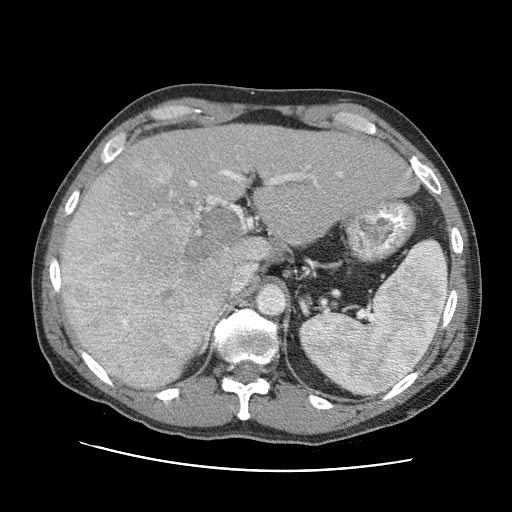
Contrast-enhanced abdominal CT (liver protocol), one axial slice; position 58 of 95 along the scan axis; reconstruction kernel STANDARD; 120 kVp; one of 2 acquisitions stored at this slice position; soft-tissue window (W 400 / L 40 HU); 2.5 mm slice thickness; 512 × 512 image matrix, field of view 360 × 360 mm. Case-level facts recorded for this patient, not image findings: diagnosis: hepatocellular carcinoma (patient treated with transarterial chemoembolisation; whether this scan precedes or follows treatment is not stated here); TNM stage (as recorded): Stage-IVA; Child-Pugh class: A; tumour differentiation: moderately differentiated; tumour nodularity: multinodular.
Annotated regions visible in this slice (semi-automatically segmented with operator editing):
- liver parenchyma outside the tumour (the mass and vessels are separate outlines, so this box may not span the whole liver): box from (x=60, y=124) to (x=416, y=388) px
- mass: (x=61, y=144)–(x=250, y=385)
- liver vessels: (x=189, y=165)–(x=410, y=325)